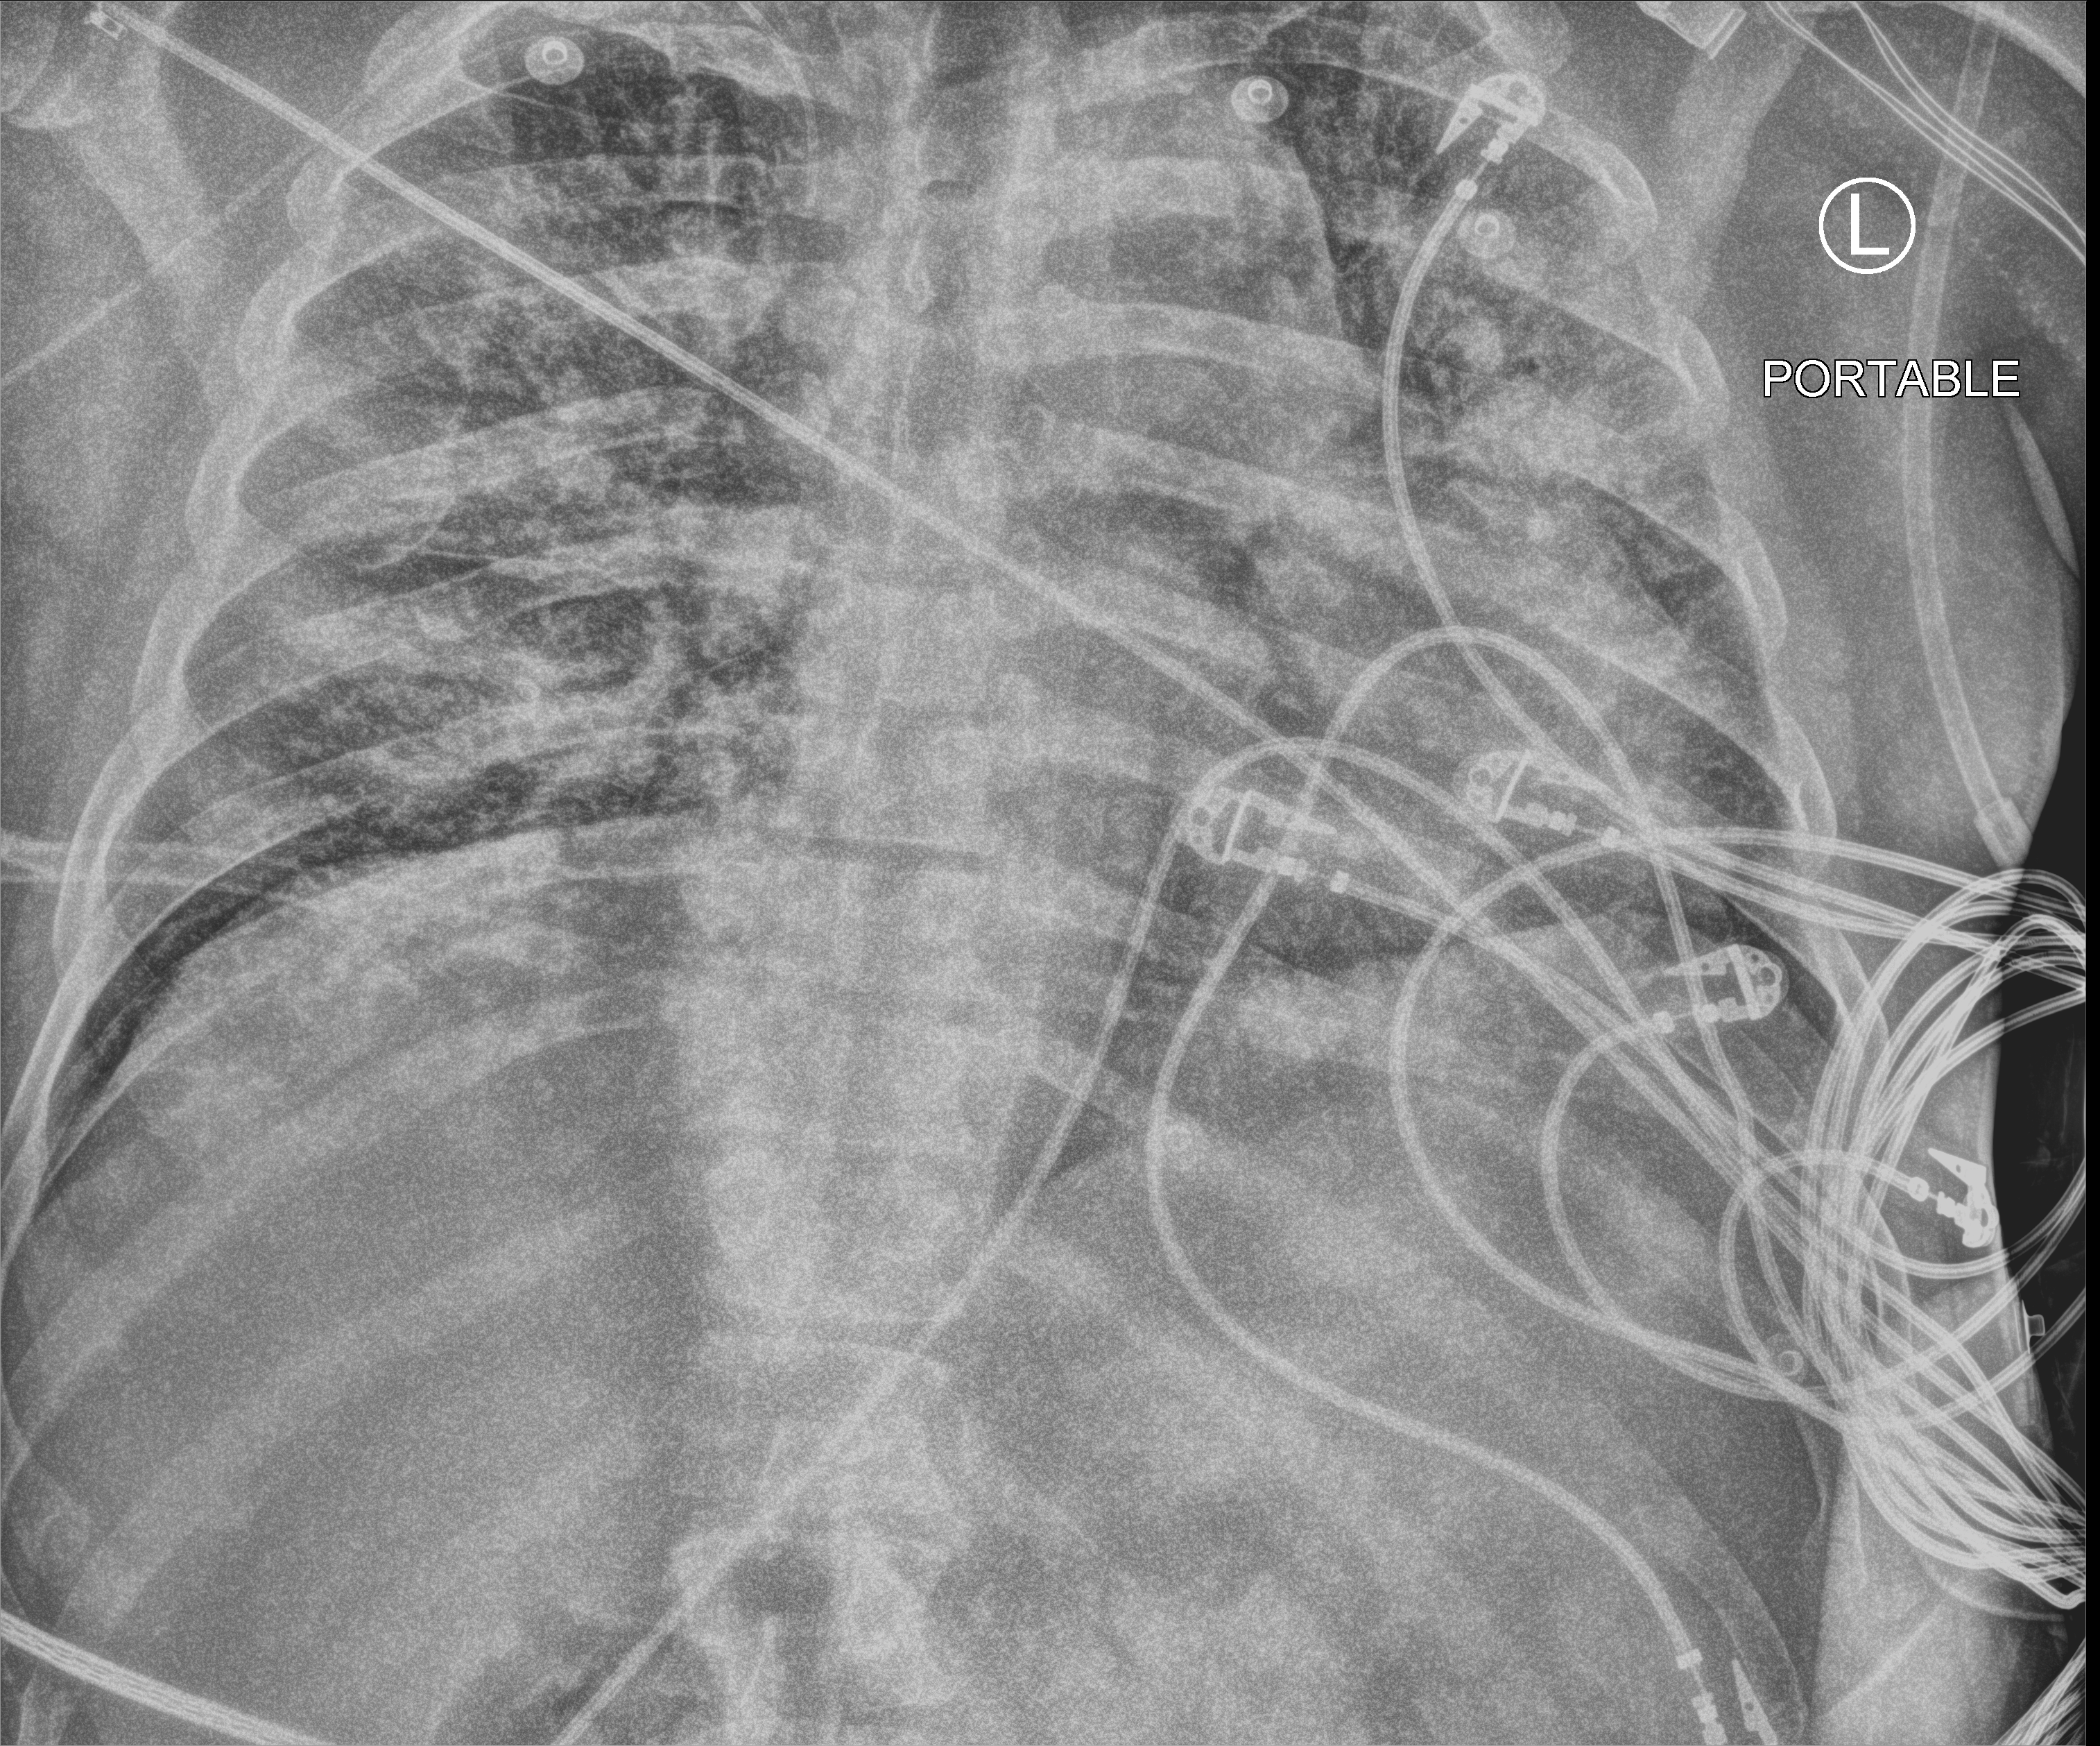
Chest X-ray (portable), anteroposterior (AP) projection. Male patient hospitalised with COVID-19, age 18–59 years.
Hospital-stay facts (about this admission, not read from this image; timing relative to this image not recorded): COPD (admission record): no; admitted to intensive care during this hospital stay: yes; mechanically ventilated during this hospital stay: yes.